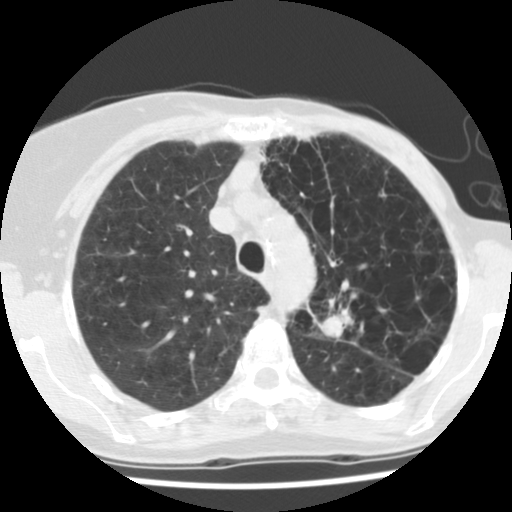
Axial slice from a low-dose chest CT screening exam, first (baseline) screen, lung window (W 1500 / L -600 HU), 2.5 mm slice thickness, standard (soft-tissue) reconstruction kernel (STANDARD). Female, age 67 years at enrolment.
Expert reader's lesion annotation, bounding box [x1, y1, x2, y2] px = [302, 283, 380, 358]. The screening reader recorded 2 non-calcified nodules or masses ≥4 mm on this exam; which of them this box marks is not recorded. Later outcome: lung cancer diagnosed 109 days after this screen — adenocarcinoma, NOS, left upper lobe, poorly differentiated (G3), stage IIB (AJCC 6th edition), 45 mm at pathology.